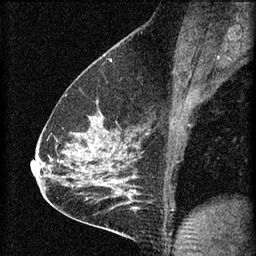
Breast MRI (dynamic contrast-enhanced), one sagittal slice; position 39 of 60 along the scan axis; 3 images stored at this slice position (order not interpretable as contrast timing); 1.5 T; TE 4.2 ms, TR 8.2 ms; 2 mm slice thickness; 256 × 256 image matrix, field of view 180 × 180 mm. Patient: female, 59 years.
Structures marked on this image (semi-automatically segmented with operator editing):
- analysis volume of interest (the breast-tissue region the enhancement analysis was run in; not a lesion): bounding box <61,104,134,161> (left, top, right, bottom; pixels)
- tumour enhancement mask (voxels above the 70 % enhancement threshold inside the analysis volume of interest): <74,134,116,151>